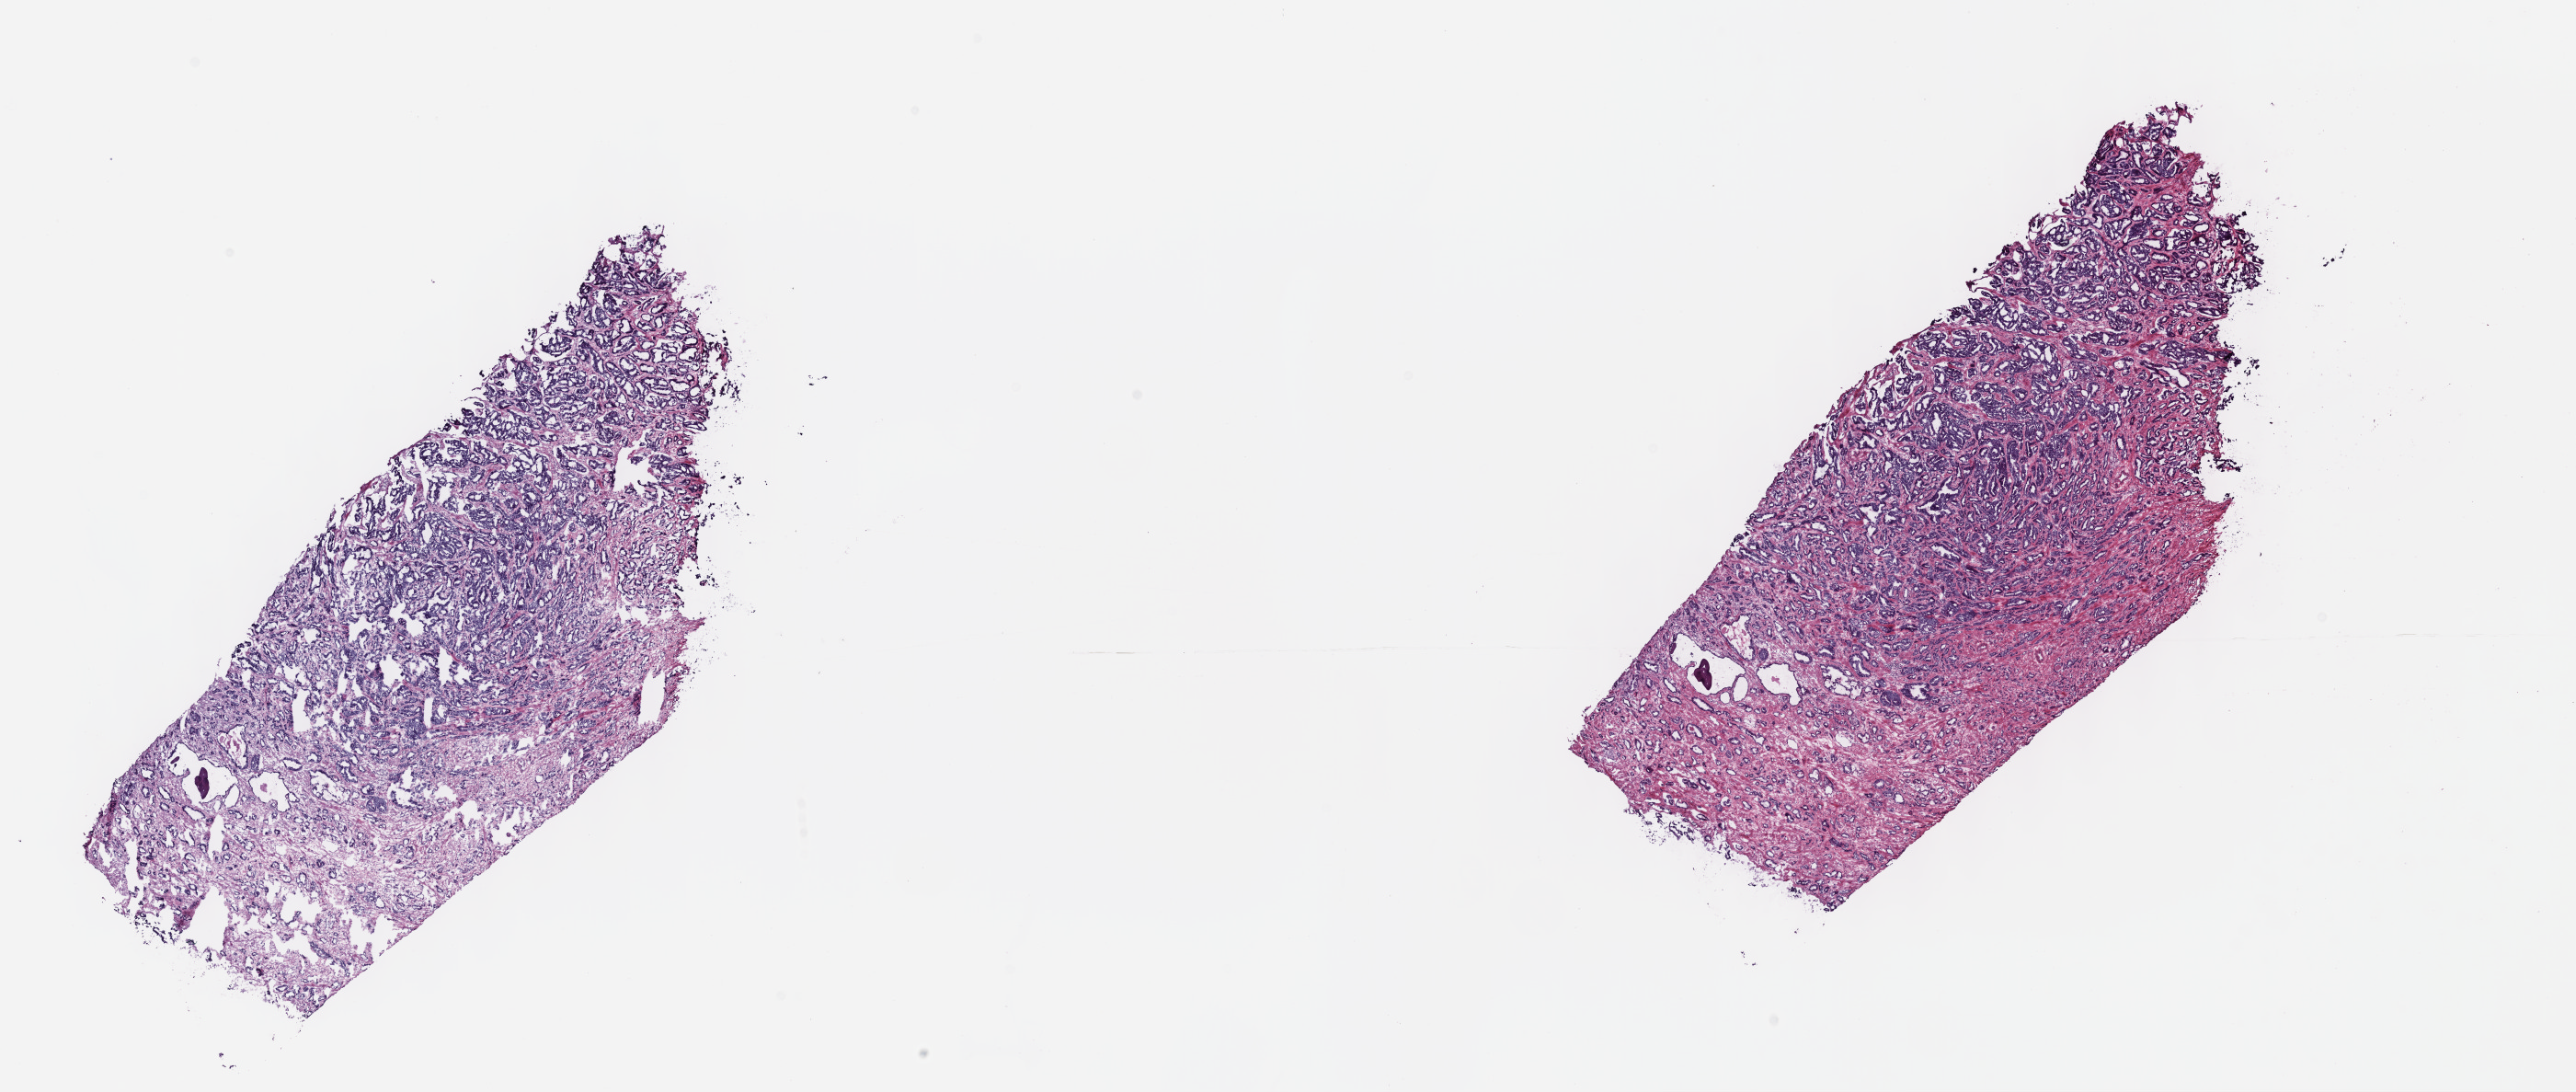
Whole-slide histology image, Hematoxylin and eosin (H&E) stained, a low-resolution overview of the entire scanned area, about 22.7 x 9.6 mm (from a 40x scan); frozen section; sample: primary tumour, prostate. Male, age 67 years at initial diagnosis. Composition of this section per pathologist review: tumour cells 70%, tumour nuclei 80%.
Histologic diagnosis: Adenocarcinoma, NOS (prostate gland).